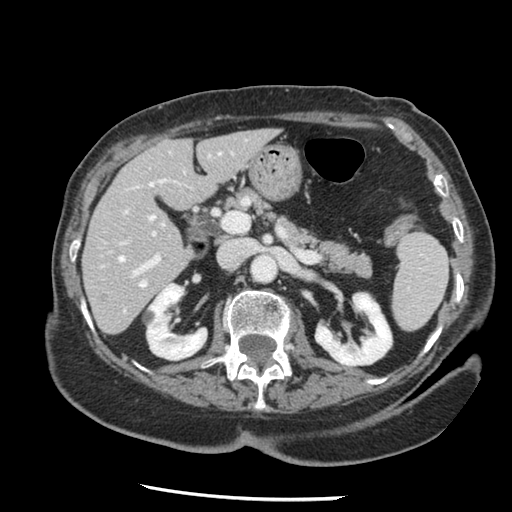
Contrast-enhanced abdominal CT, one axial slice. Position 69 of 148 along the scan axis. Intravenous contrast given. Soft-tissue window (W 400 / L 40 HU). 512 × 512 image matrix, field of view 330 × 330 mm. Female patient, age 85 years. Case-level facts recorded for this patient, not image findings: diagnosis: colorectal cancer liver metastases, imaged before liver resection; multiple liver metastases: no; largest metastasis: 0.9 cm; disease in both lobes: no.
Outlined on this slice (outlined manually by an expert reader):
- hepatic veins: bounding box (x1, y1, x2, y2) in pixels: (119, 184, 153, 287)
- liver: (83, 130, 277, 334)
- planned liver remnant (the part of the liver to remain after resection): (83, 130, 277, 331)
- portal vein (with intrahepatic branches): (124, 211, 161, 278)
- liver metastasis: (102, 294, 108, 300)